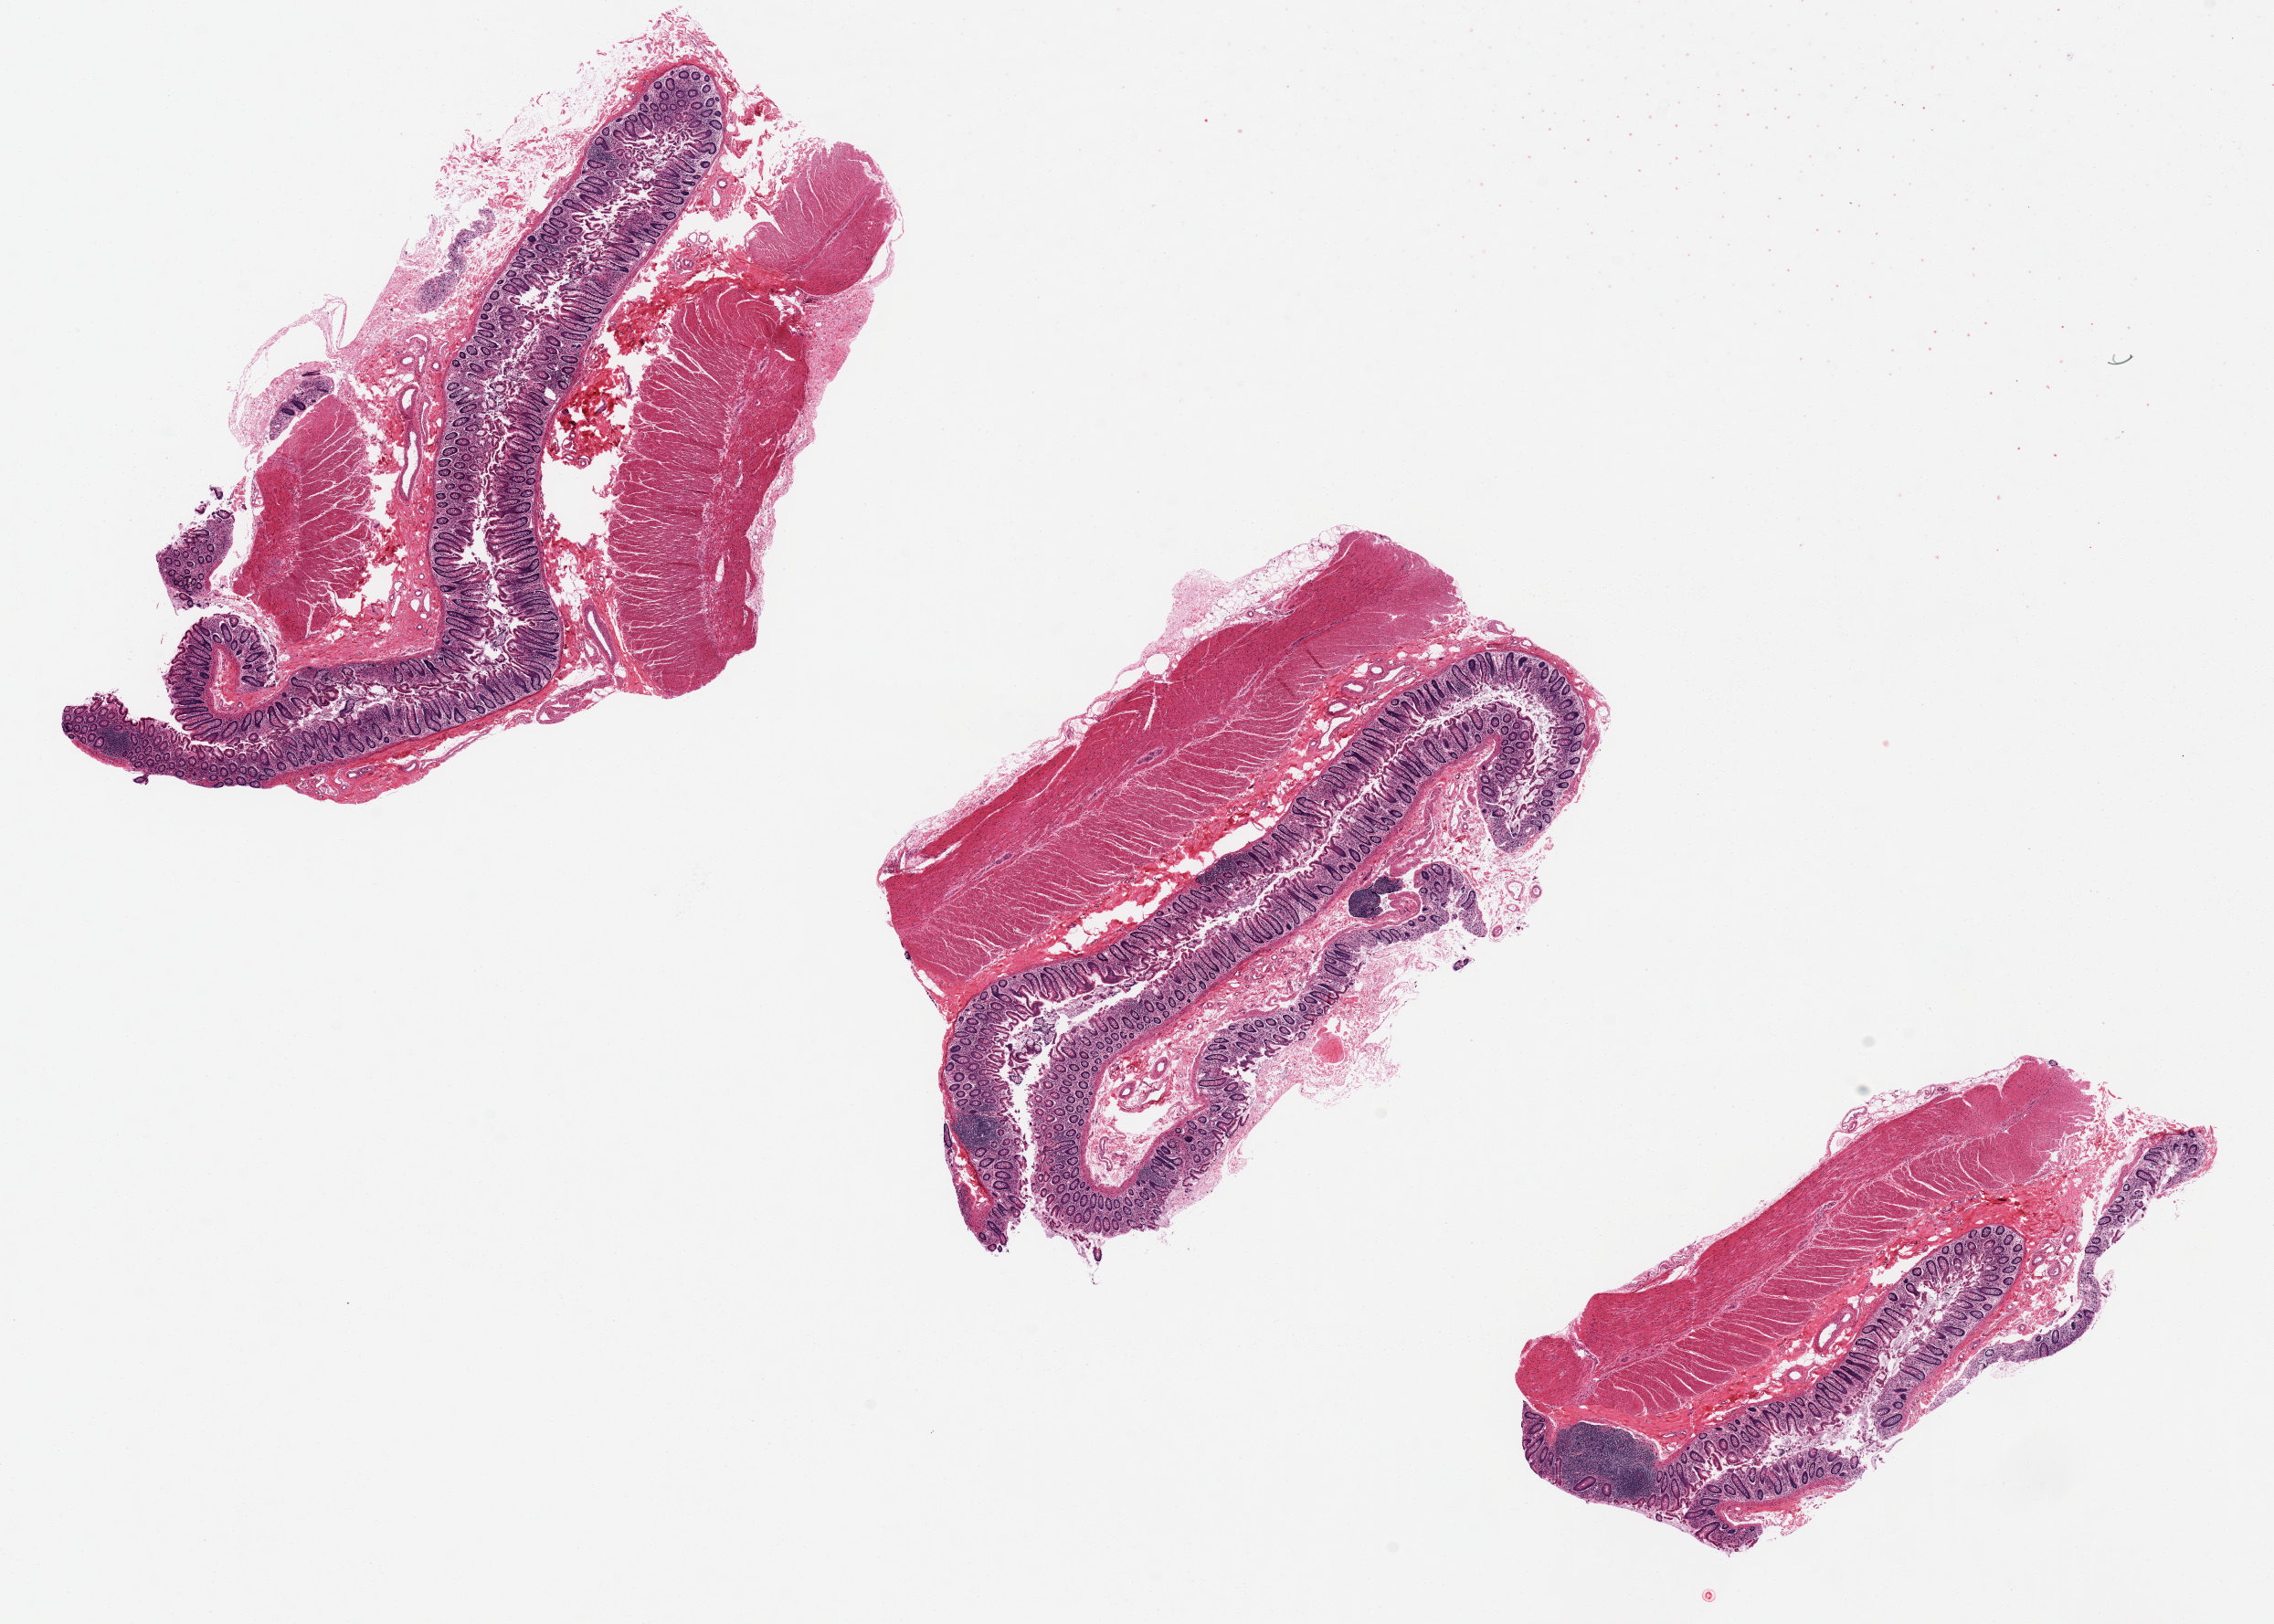
Digitized H&E-stained section, whole scanned area (about 19.7 x 14.1 mm) shown as a low-resolution overview; PAXgene-fixed, paraffin-embedded tissue; target tissue: transverse colon; donor tissue sample. Male donor.
Reviewer comment on this tissue sample: remarkably well preserved; minimal superficial autolysis.